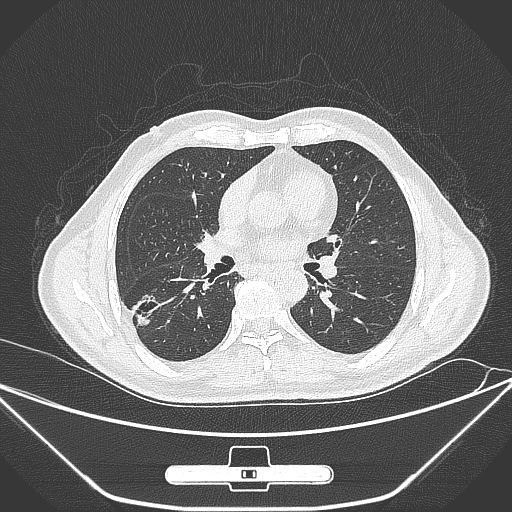
Chest CT, one axial slice. Slice 150 of 310 in the series (ordered by position). 120 kVp. Lung window (W 1500 / L -600 HU). 1 mm slice thickness. 512 × 512 image matrix, field of view 398 × 398 mm. Patient: male, 71 years. Case-level facts recorded for this patient, not image findings: clinical TNM (as recorded): T1c N0 M0; histopathological grade: G2.
Outlined on this slice (bounding box drawn by a radiologist):
- lung tumour (recorded histology: adenocarcinoma): bounding box (x1, y1, x2, y2) in pixels: (126, 293, 163, 330)